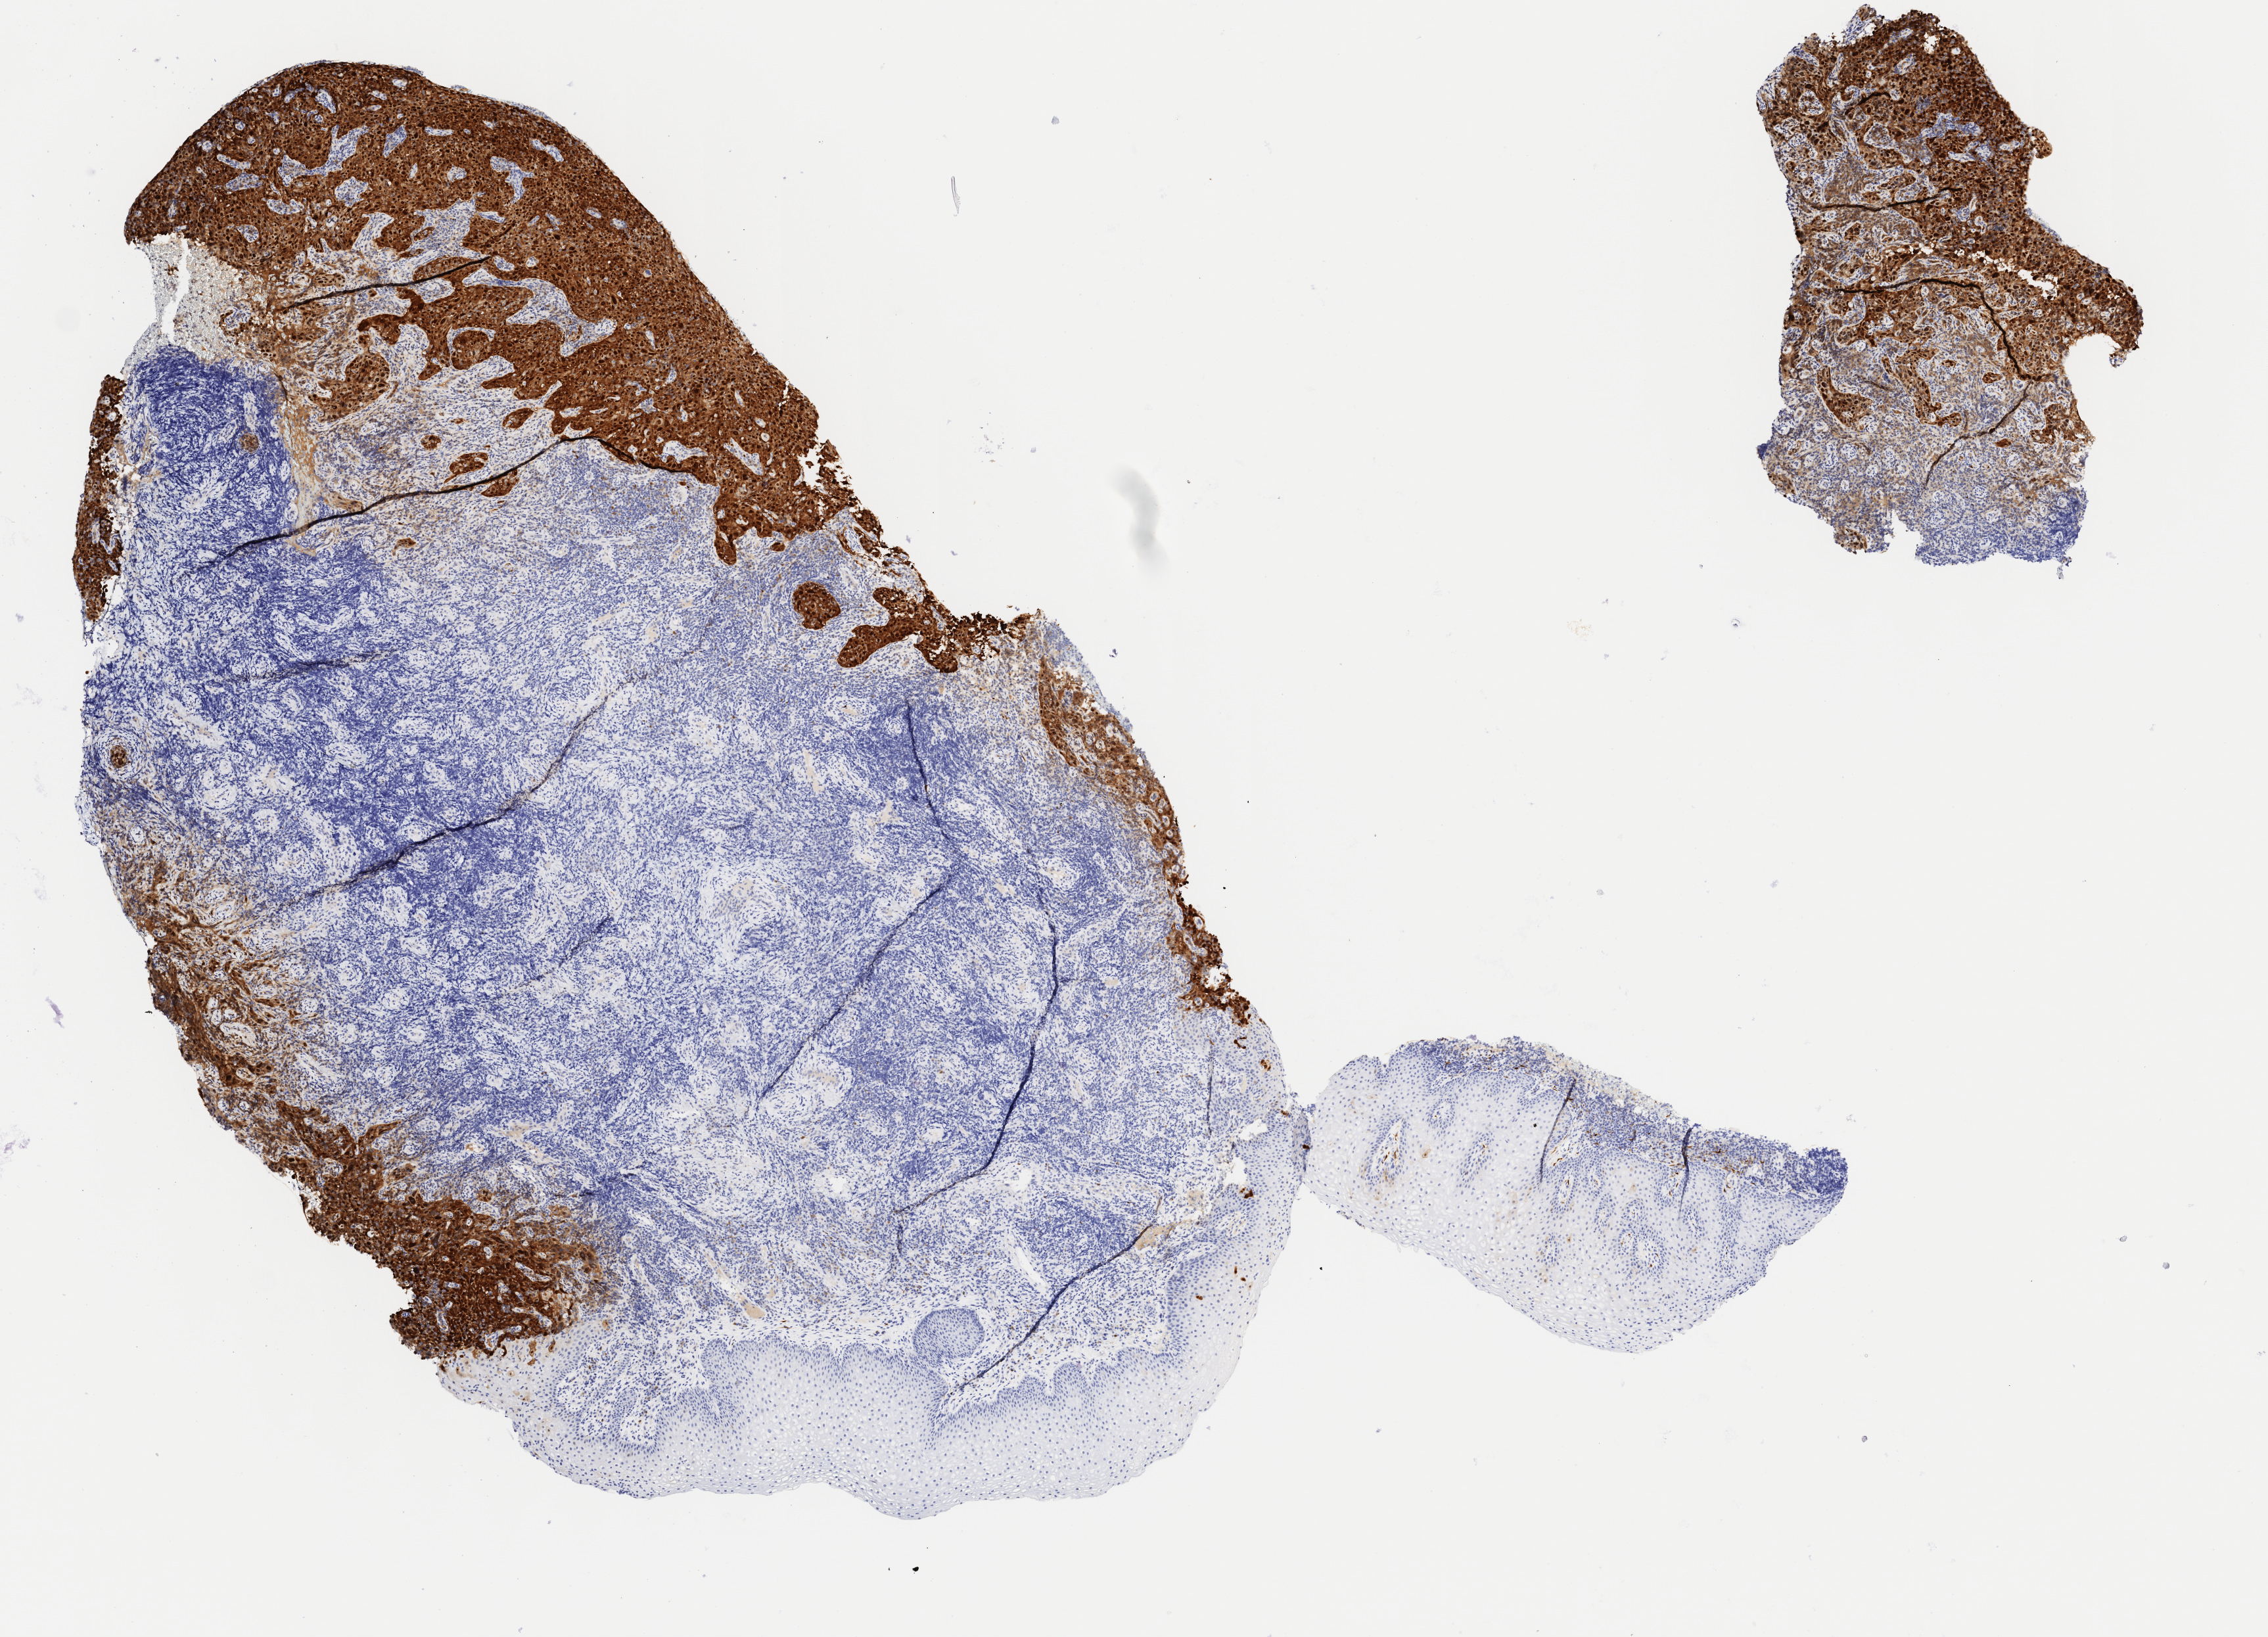
IHC for p16 (p16INK4a), whole-slide image — low-resolution overview of the scanned area, about 6.9 x 5.0 mm, tumor tissue, anatomic site: cervix. Patient female; aged 29.
Diagnosis: Squamous cell carcinoma, large cell, nonkeratinizing, NOS.